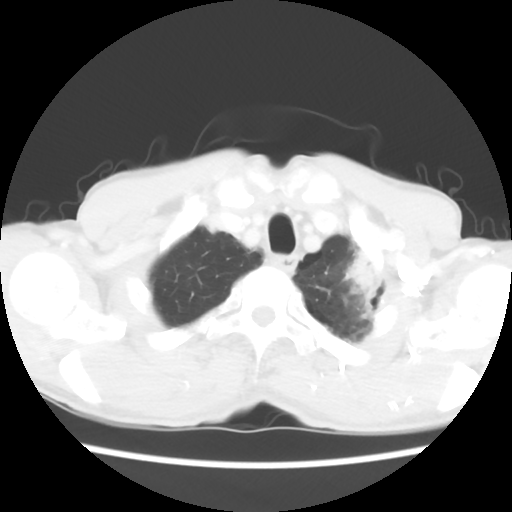
Chest CT, one axial slice; slice 54 of 60 in the series (ordered by position); reconstruction kernel STANDARD; 120 kVp; lung window (W 1500 / L -600 HU); 5 mm slice thickness; 512 × 512 image matrix, field of view 308 × 308 mm. Patient: male, 64 years. Case-level facts recorded for this patient, not image findings: clinical TNM (as recorded): T3 N3 M0.
Structures marked on this image (rectangle marked by the reading radiologist):
- lung tumour (recorded histology: adenocarcinoma): bounding box [x1, y1, x2, y2] px = [342, 245, 388, 314]